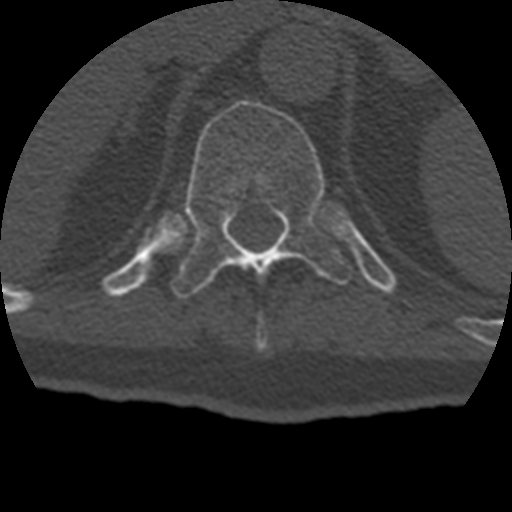
CT including the spine, one axial slice. Position 200 of 399 along the scan axis. Reconstruction kernel STANDARD. Bone window (W 1800 / L 400 HU). 1.25 mm slice thickness. 512 × 512 image matrix. Patient age 69 years. Case-level facts recorded for this patient, not image findings: primary cancer: prostate.
Outlined on this slice (semi-automatically segmented with operator editing):
- T10 vertebra: bounding box <256,332,267,348> (left, top, right, bottom; pixels)
- T11 vertebra: <171,100,353,298>